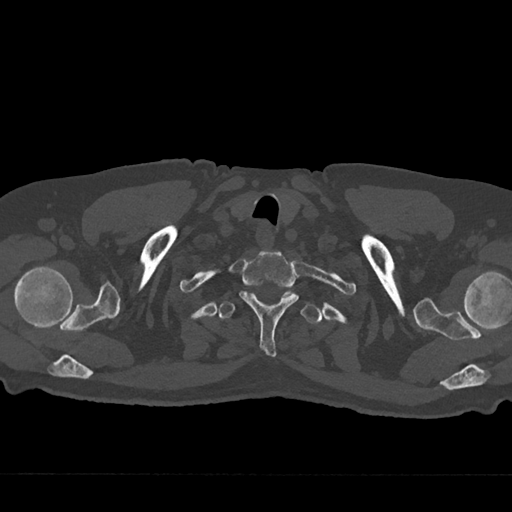
CT including the spine, one axial slice. Slice 649 of 797 in the series (ordered by position). Reconstruction kernel Br40s/3. Bone window (W 1800 / L 400 HU). 0.5 mm slice thickness. 512 × 512 image matrix, field of view 377 × 377 mm. Male patient, age 75 years. Case-level facts recorded for this patient, not image findings: primary cancer: renal; vertebrae with lytic lesions (as recorded): T4.
Structures marked on this image (semi-automatic segmentation, software-assisted and operator-edited):
- T1 vertebra: bounding box <239,250,299,356> (left, top, right, bottom; pixels)
- T2 vertebra: <218,290,322,324>